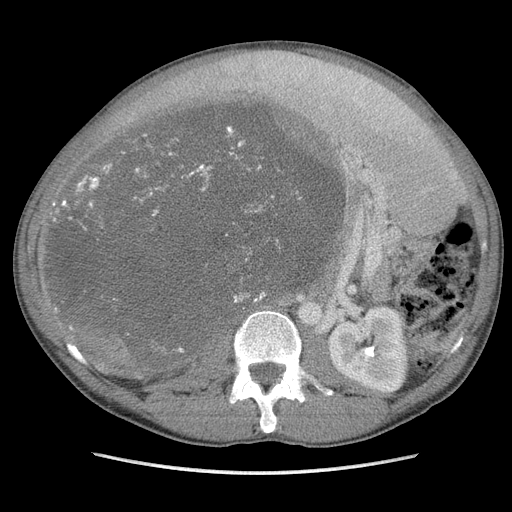
Contrast-enhanced abdominal CT, one axial slice; soft-tissue window (W 400 / L 40 HU); 5 mm slice thickness; 512 × 512 image matrix, field of view 360 × 360 mm. Male patient. Case-level facts recorded for this patient, not image findings: diagnosis: adrenocortical carcinoma; tumour side: right adrenal; Ki-67 index: 13 %; stage (as recorded): 3.
Annotated regions visible in this slice (semi-automatic segmentation, software-assisted and operator-edited):
- mass: bounding box (x1, y1, x2, y2) in pixels: (52, 100, 340, 372)